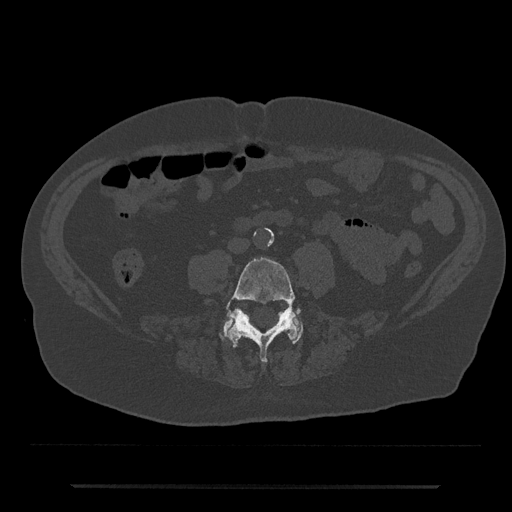
CT including the spine, one axial slice. Reconstruction kernel Br40s/3. 120 kVp. Bone window (W 1800 / L 400 HU). 0.5 mm slice thickness. 512 × 512 image matrix, field of view 434 × 434 mm. Patient: male, 80 years. From the clinical record (not read from this slice): primary cancer: prostate; vertebrae with lytic lesions (as recorded): L1, T11.
Outlined on this slice (semi-automatic segmentation, software-assisted and operator-edited):
- L4 vertebra: bounding box [x1, y1, x2, y2] px = [226, 257, 311, 363]
- L5 vertebra: [220, 316, 303, 343]